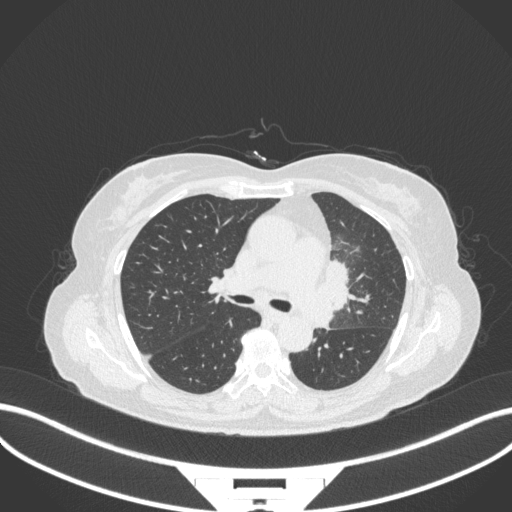
Chest CT, one axial slice. Slice 205 of 382 in the series (ordered by position). Reconstruction kernel B31f. 120 kVp. Lung window (W 1500 / L -600 HU). 1 mm slice thickness. 512 × 512 image matrix, field of view 400 × 400 mm. Female patient, age 64 years. From the clinical record (not read from this slice): clinical TNM (as recorded): T2a N2 M0.
Structures marked on this image (rectangle marked by the reading radiologist):
- lung tumour (recorded histology: adenocarcinoma): bounding box <308,250,360,335> (left, top, right, bottom; pixels)